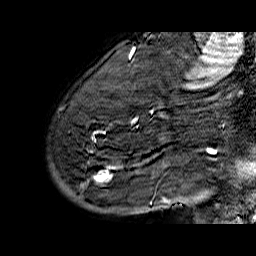
Breast MRI (dynamic contrast-enhanced), one sagittal slice; position 49 of 60 along the scan axis; dynamic contrast-enhanced series, time point 2 of 6 at this slice position (early post-contrast); 1.5 T; TE 6.5 ms, TR 32.9 ms; 256 × 256 image matrix, field of view 200 × 200 mm. Female patient. From the clinical record (not read from this slice): setting: breast cancer imaged before/during neoadjuvant chemotherapy; receptor status: HR-positive, HER2-negative.
Annotated regions visible in this slice (semi-automatically segmented with operator editing):
- analysis volume of interest (the breast-tissue region the enhancement analysis was run in; not a lesion): bounding box [x1, y1, x2, y2] px = [49, 74, 176, 210]
- tumour enhancement mask (voxels above the 100 % enhancement threshold inside the analysis volume of interest): [93, 168, 109, 181]